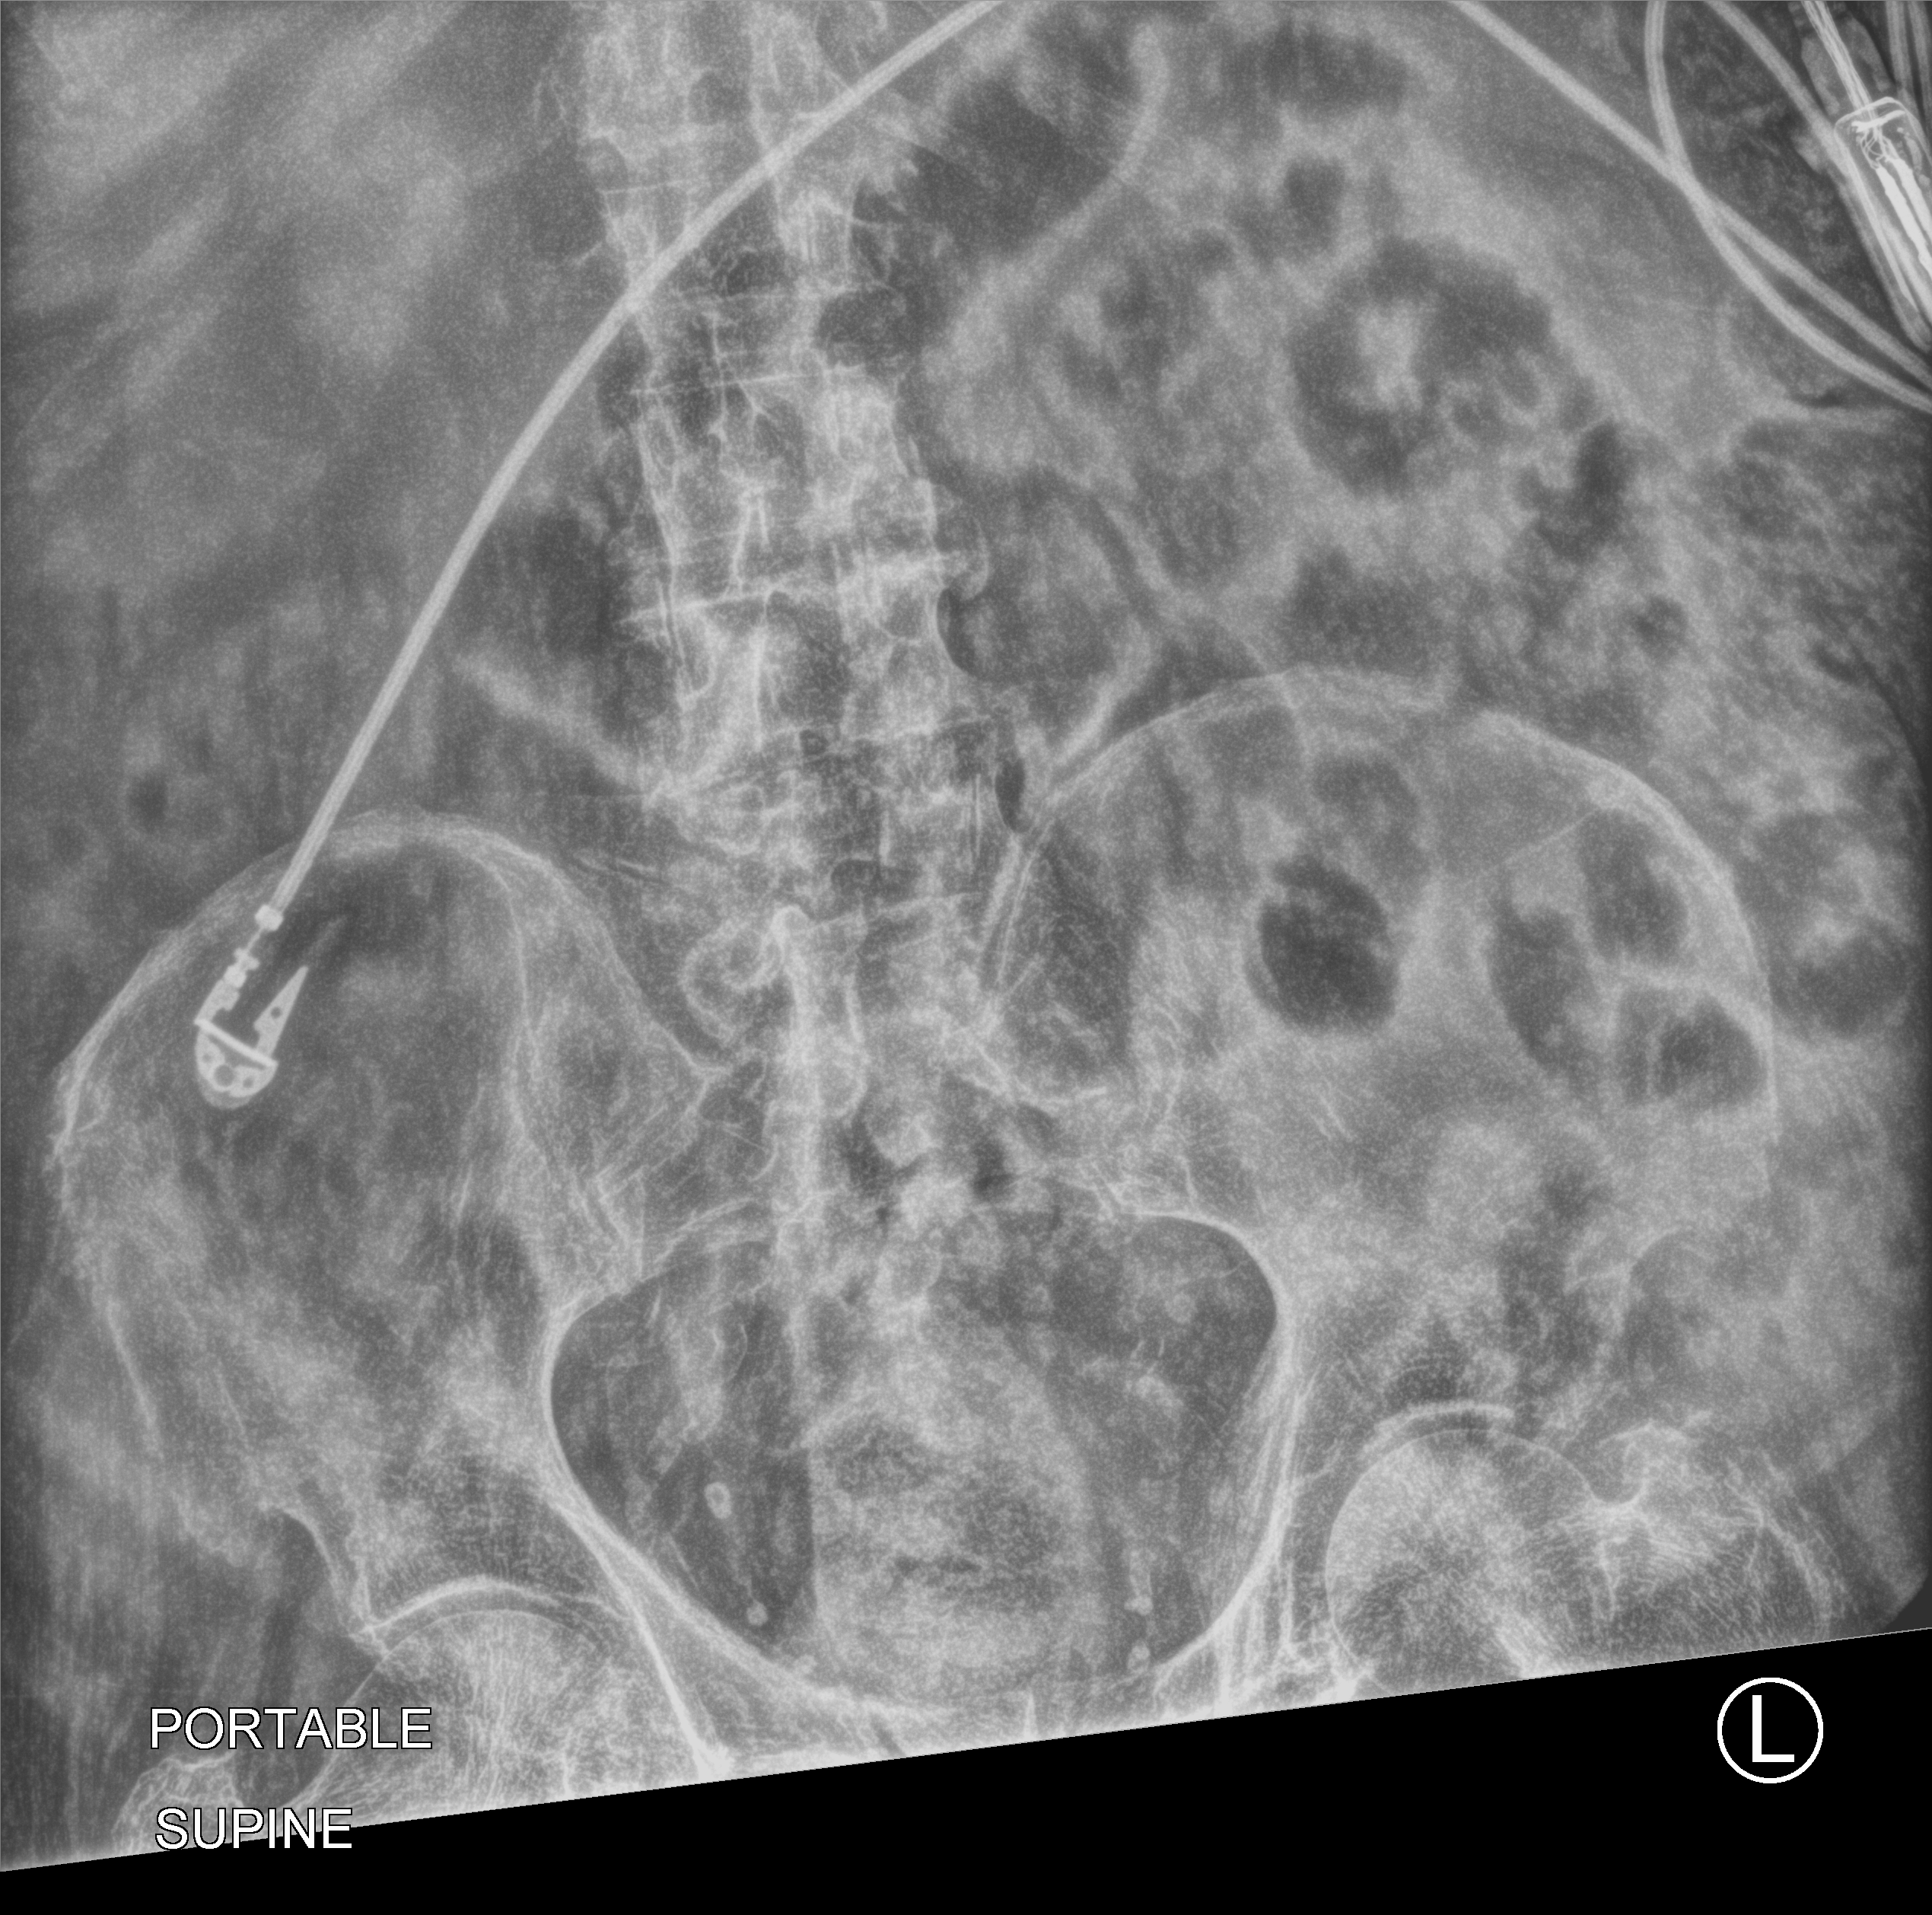
Abdomen X-ray (portable), anteroposterior (AP) projection. Patient hospitalised with COVID-19; male, aged 75–90 years.
Hospital-stay facts (about this admission, not read from this image; timing relative to this image not recorded): chronic kidney disease (admission record): no; admitted to intensive care during this hospital stay: no; mechanically ventilated during this hospital stay: no.